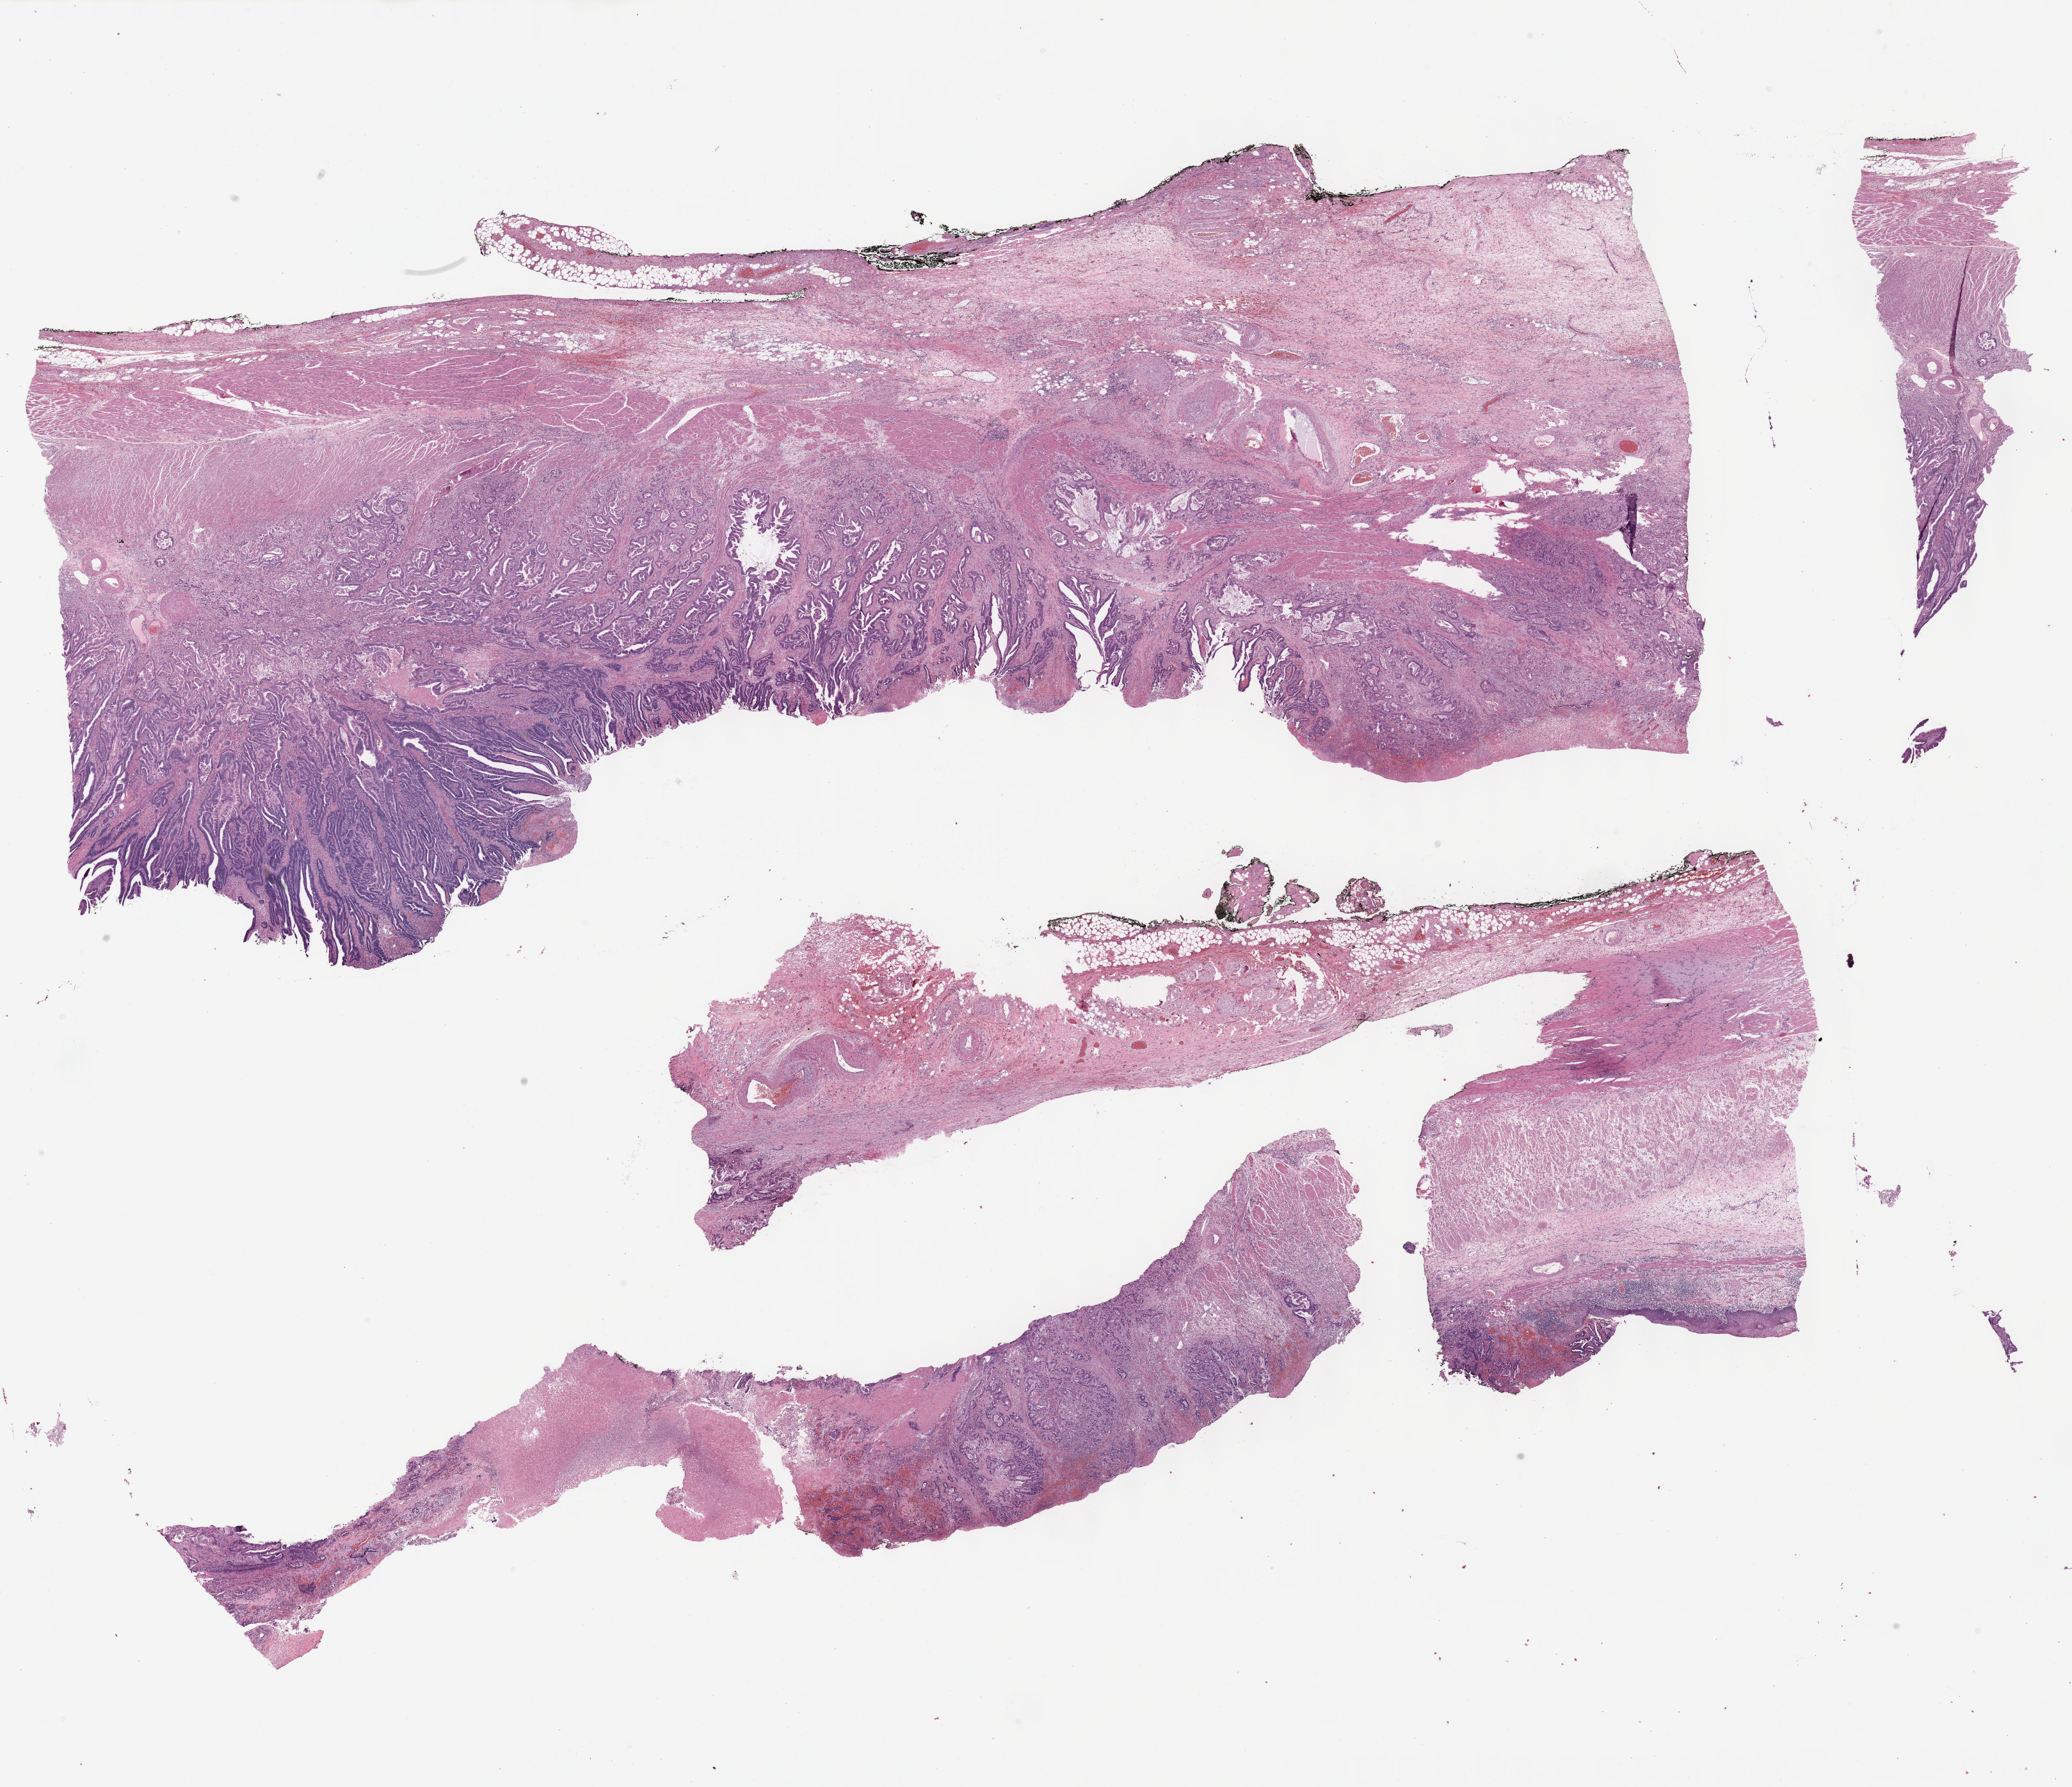
Digitized H&E tissue section (whole slide) — low-resolution overview of the scanned area, about 26.2 x 22.6 mm. FFPE section. Stomach, primary tumour sample. Male, age 68 years at initial diagnosis. Histologic grade: G2 (moderately differentiated).
Diagnosis: Adenocarcinoma, intestinal type (cardia, NOS). AJCC pathologic stage: IIA (7th edition). Lymph nodes positive (case pathology): 0 of 19 examined.